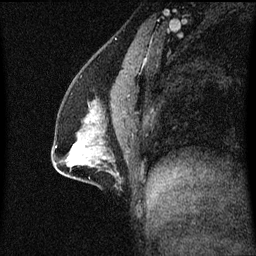
Breast MRI (dynamic contrast-enhanced), one sagittal slice. Dynamic contrast-enhanced series, image 2 of 3 at this slice position (ordered by acquisition). 1.5 T. TE 4.2 ms, TR 8.4 ms. 256 × 256 image matrix, field of view 200 × 200 mm. Patient: female, 41 years. From the clinical record (not read from this slice): setting: breast cancer imaged before/during neoadjuvant chemotherapy; receptor status: triple-negative.
Annotated regions visible in this slice (semi-automatic segmentation, software-assisted and operator-edited):
- analysis volume of interest (the breast-tissue region the enhancement analysis was run in; not a lesion): bounding box <52,104,125,175> (left, top, right, bottom; pixels)
- tumour enhancement mask (voxels above the 70 % enhancement threshold inside the analysis volume of interest): <73,146,76,151>